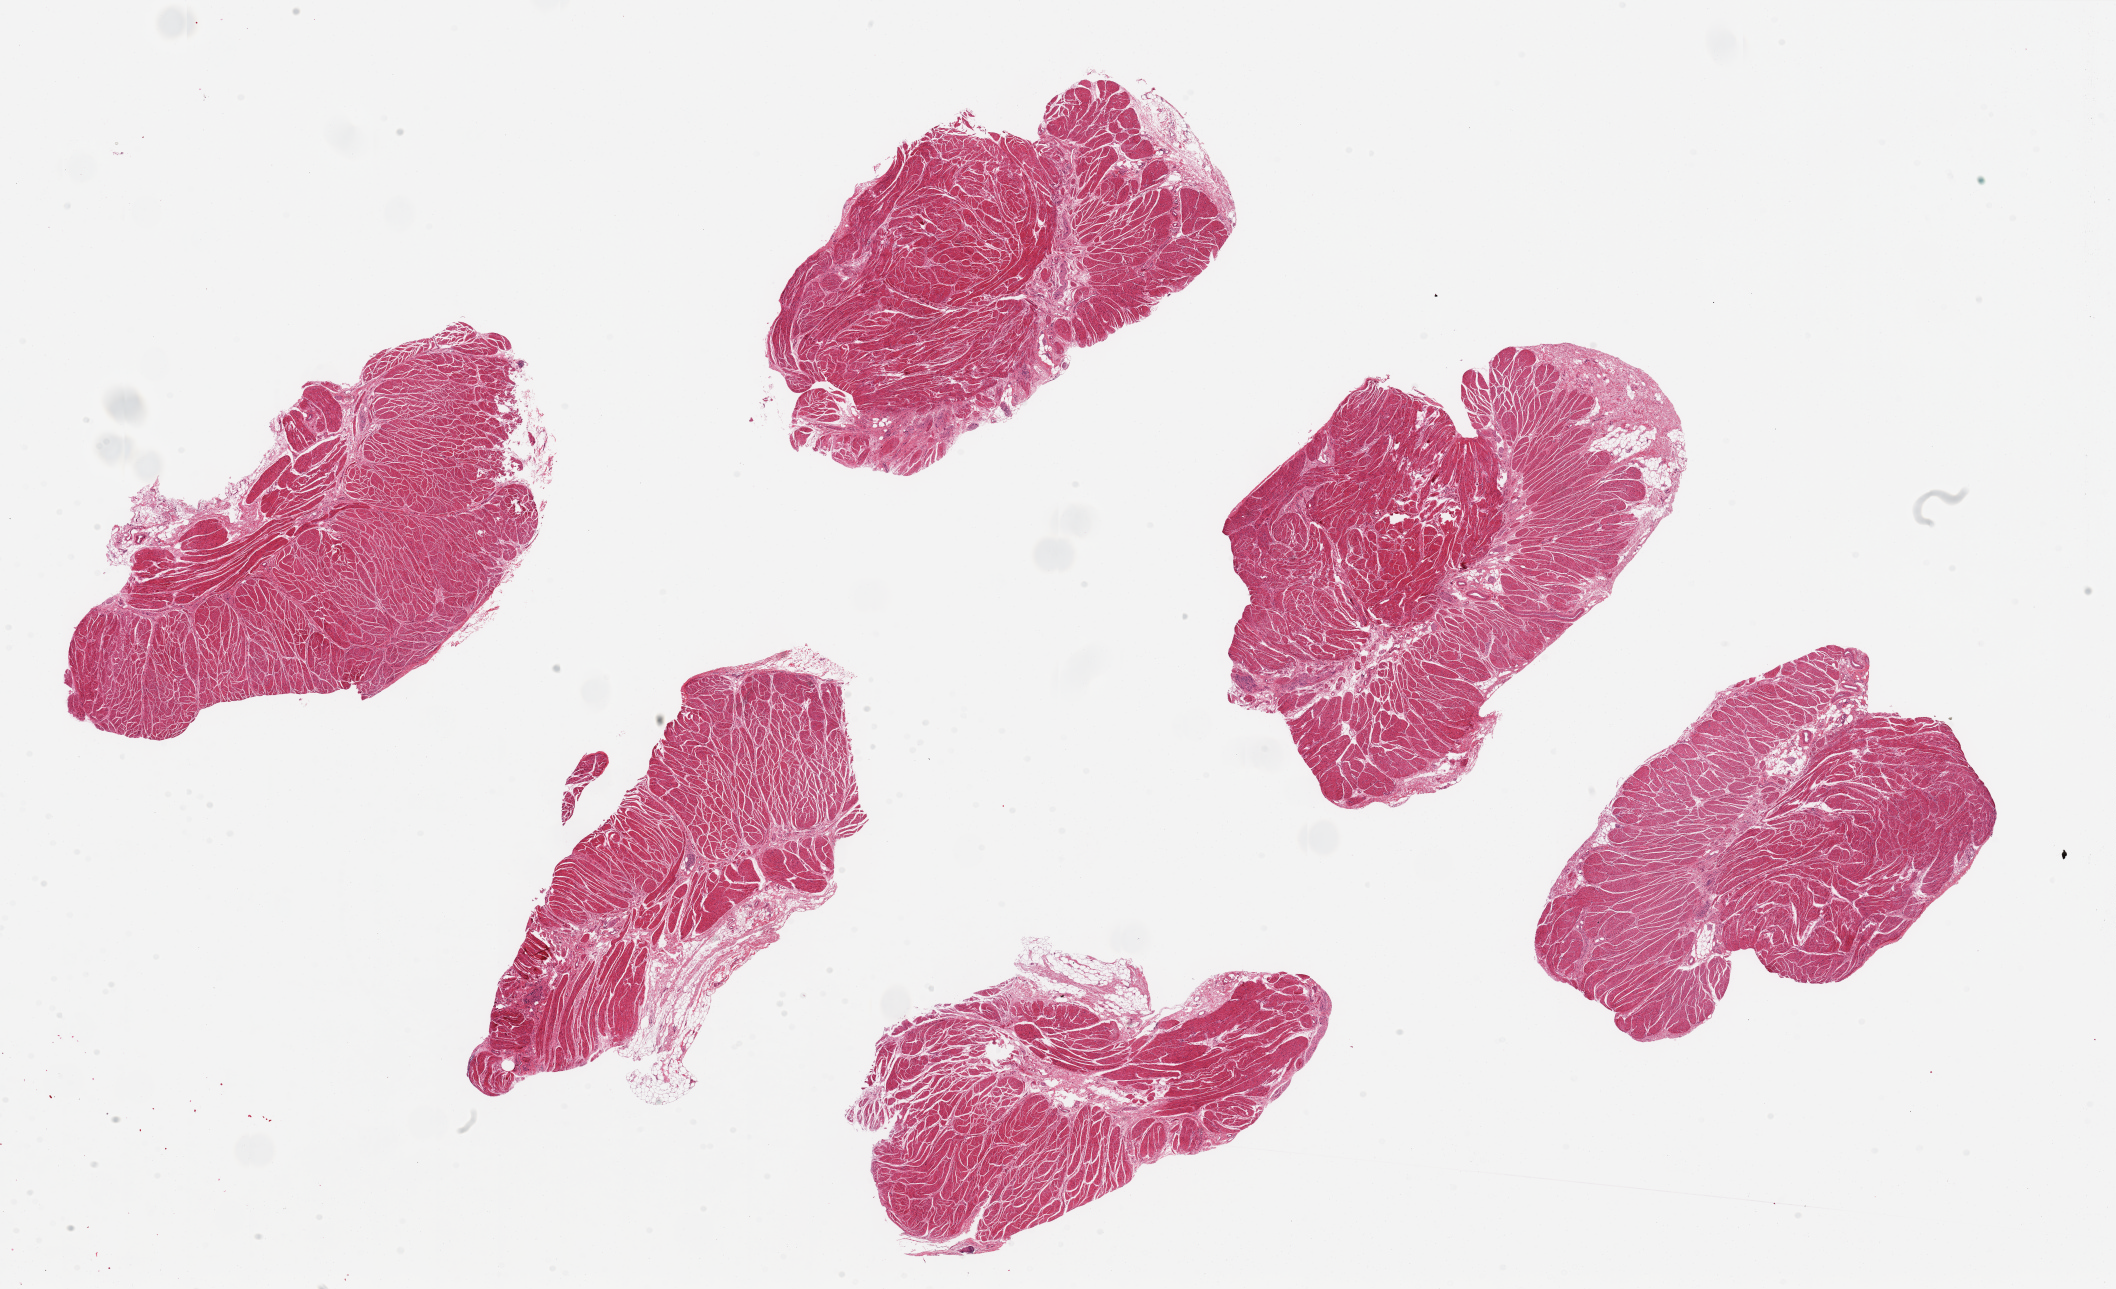
Haematoxylin and eosin whole-slide image — whole scanned area (about 33.5 x 20.4 mm) shown as a low-resolution overview; PAXgene-fixed, paraffin-embedded tissue; sampled site (target tissue): esophageal muscle; tissue donor sample. Donor sex: male.
• reviewer comment on this tissue sample: 6 ~8x4mm pieces